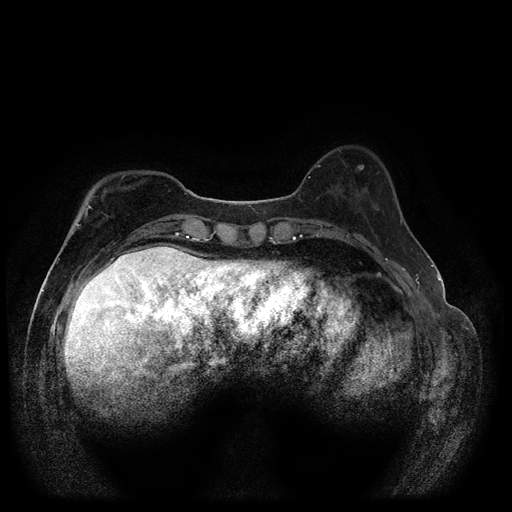
Breast MRI (dynamic contrast-enhanced, multi-phase), one axial slice. Slice 31 of 116 in the series (ordered by position). Dynamic contrast-enhanced series, time point 2 of 5 at this slice position (early post-contrast). 1.5 T. TE 2.6 ms, TR 5.4 ms. 512 × 512 image matrix, field of view 340 × 340 mm. Female patient, age 51 years.
Structures marked on this image (semi-automatically segmented with operator editing):
- breast lesion (labelled benign in the annotation): box from (x=356, y=164) to (x=365, y=172) px